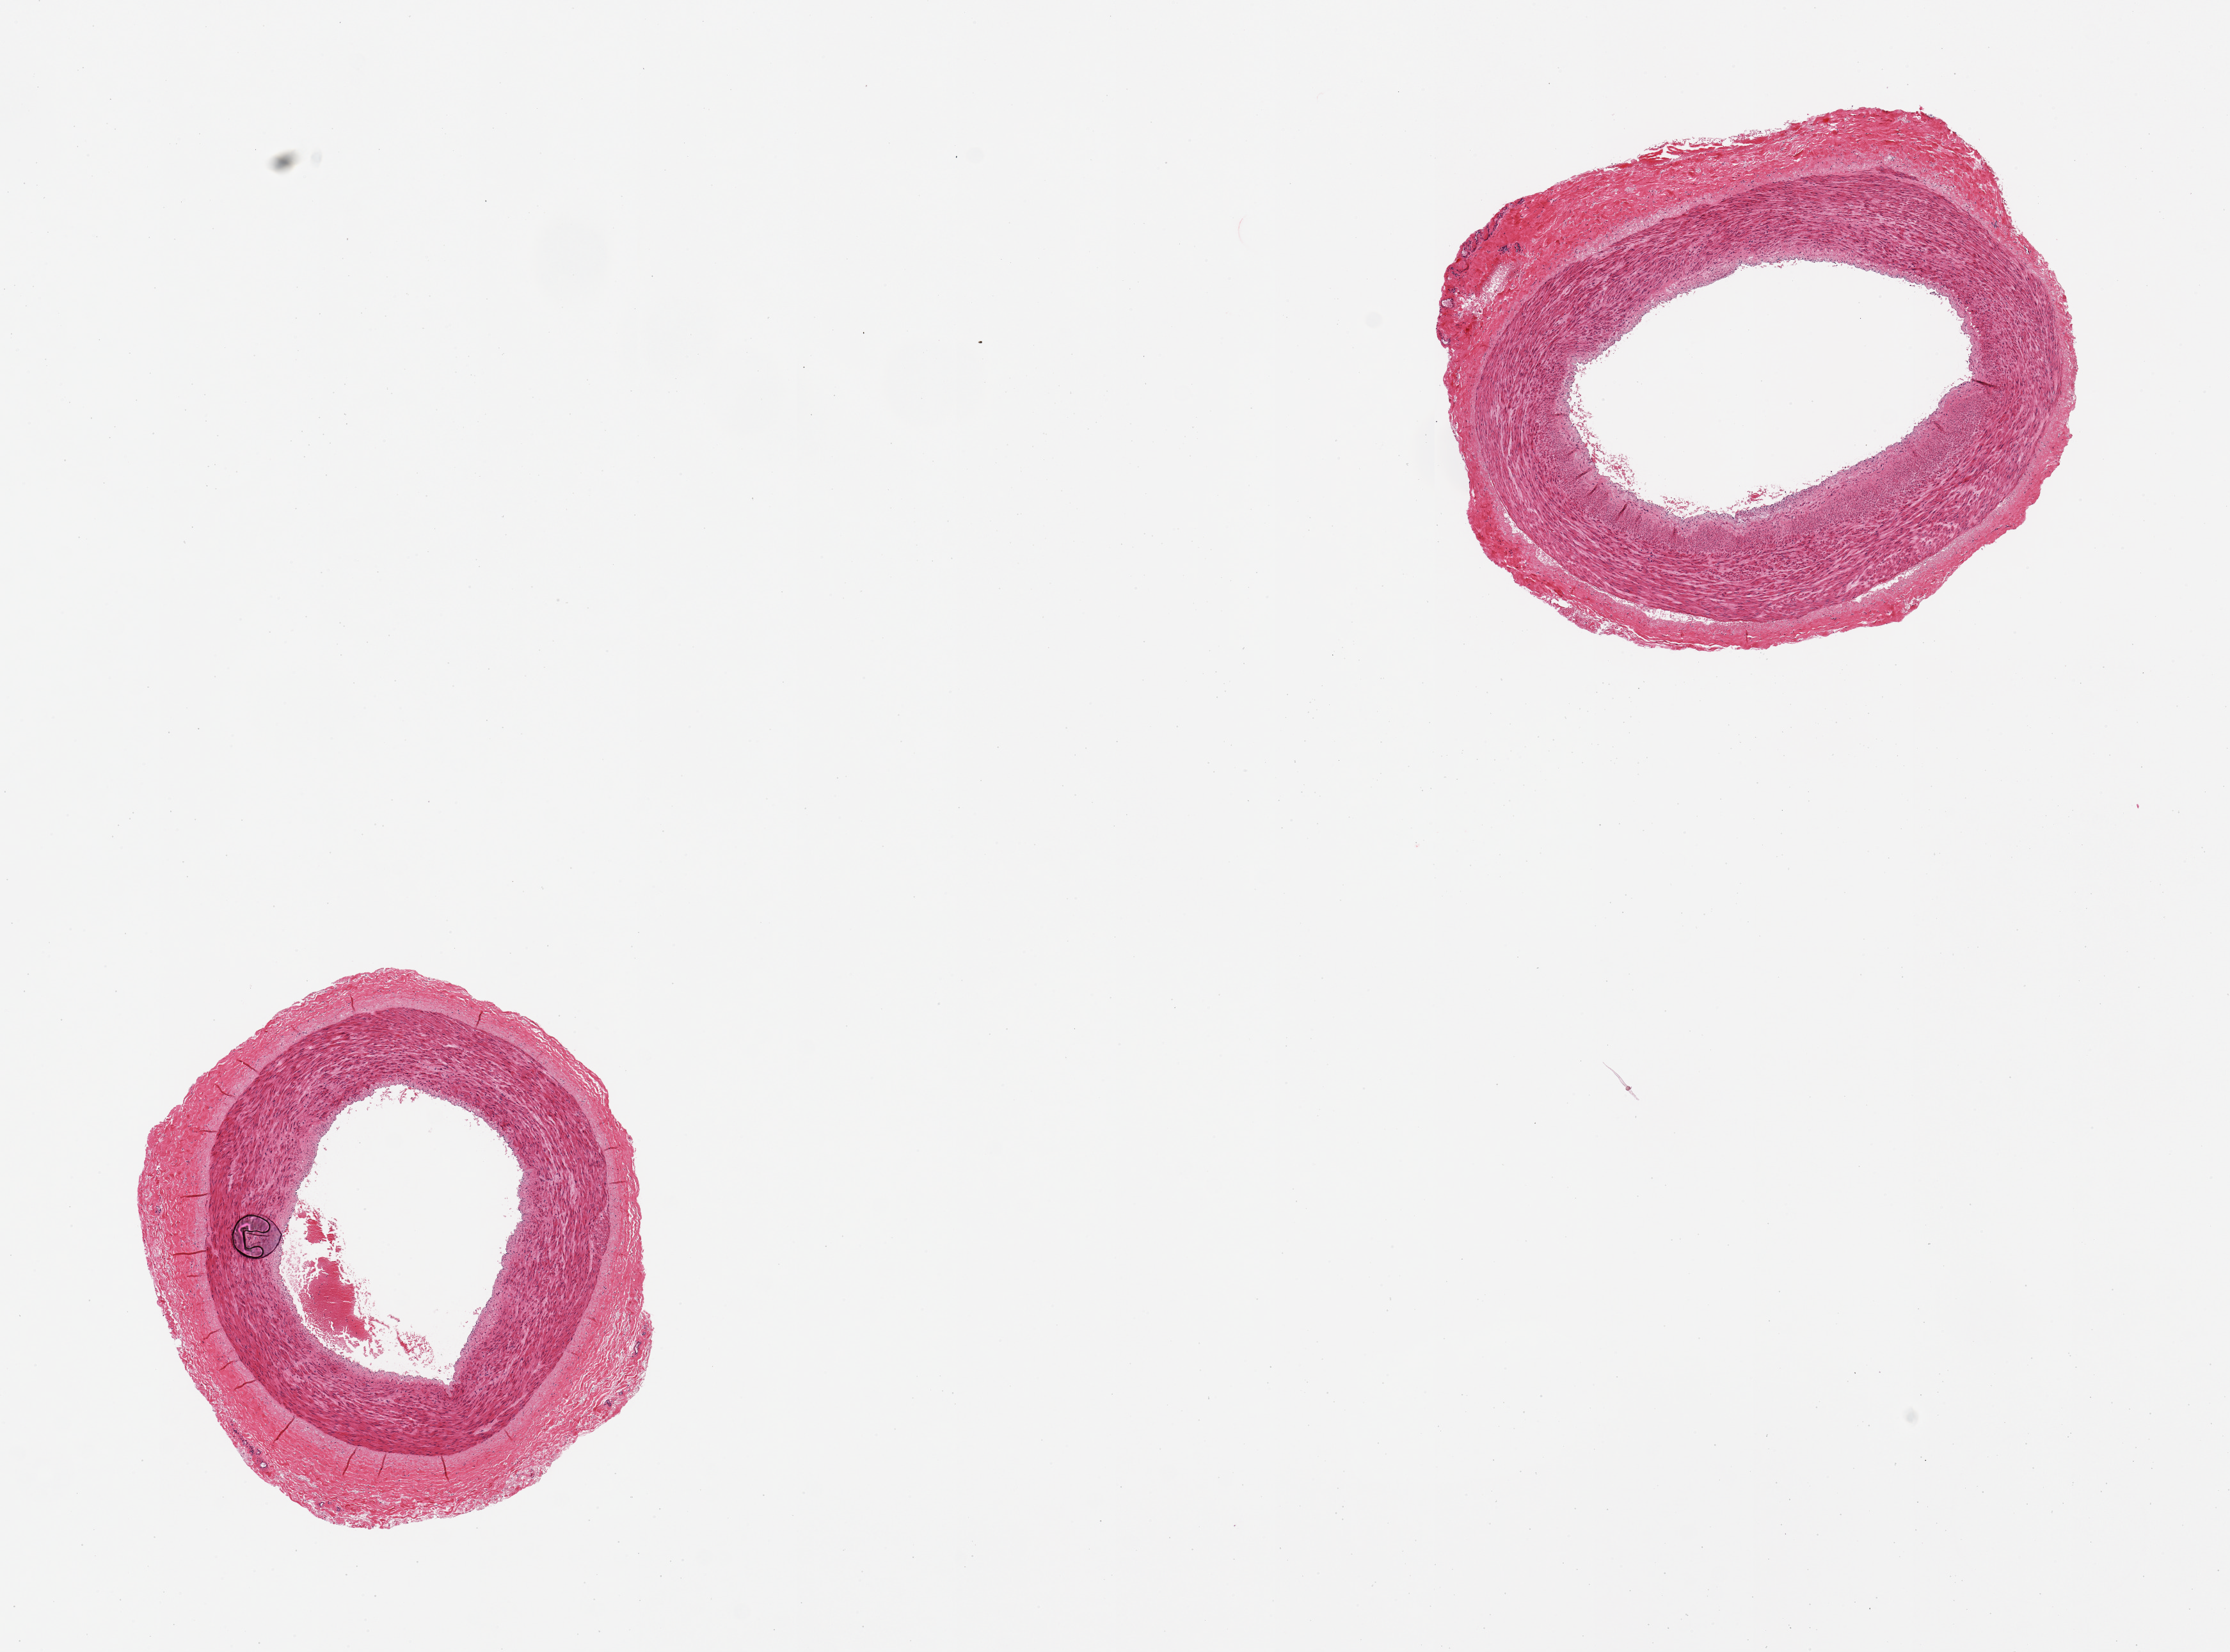
Whole-slide image, H&E stain, brightfield, whole scanned area (about 13.8 x 10.2 mm) shown as a low-resolution overview; PAXgene-fixed, paraffin-embedded tissue; section of tibial artery (target tissue); donor tissue sample. Donor: male.
• pathologist's review note for this sample: 2 pieces, 3x3 & 4x3mm; Well trimmed; Layers